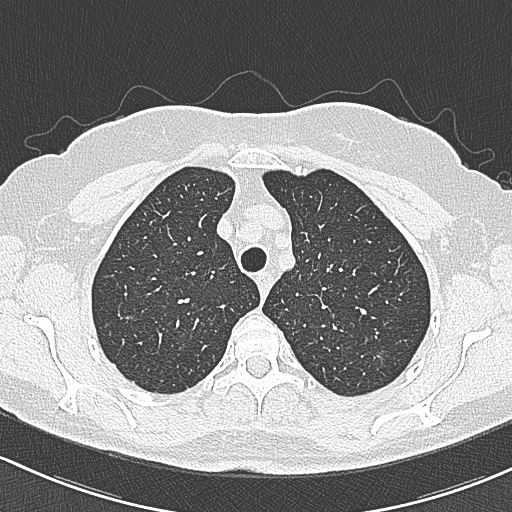
Chest CT (low-dose screening protocol), one axial image. First (baseline) screen. Lung window (W 1500 / L -600 HU). 1 mm slice thickness. 120 kVp. Slice 61 of 312 in the series. 512 × 512 image matrix. Female, age 65 years at enrolment.
Lesion marked by an expert reader, box from (x=368, y=346) to (x=404, y=380) px. The screening reader recorded 3 non-calcified nodules or masses ≥4 mm on this exam; which of them this box marks is not recorded. Official screen result: positive, change unspecified: nodule(s) >= 4 mm or enlarging nodule(s), mass(es), or other non-specific abnormalities suspicious for lung cancer. Later outcome: lung cancer diagnosed 390 days after this screen — bronchiolo-alveolar carcinoma, non-mucinous, left upper lobe, stage IA (AJCC 6th edition), 10 mm at pathology.